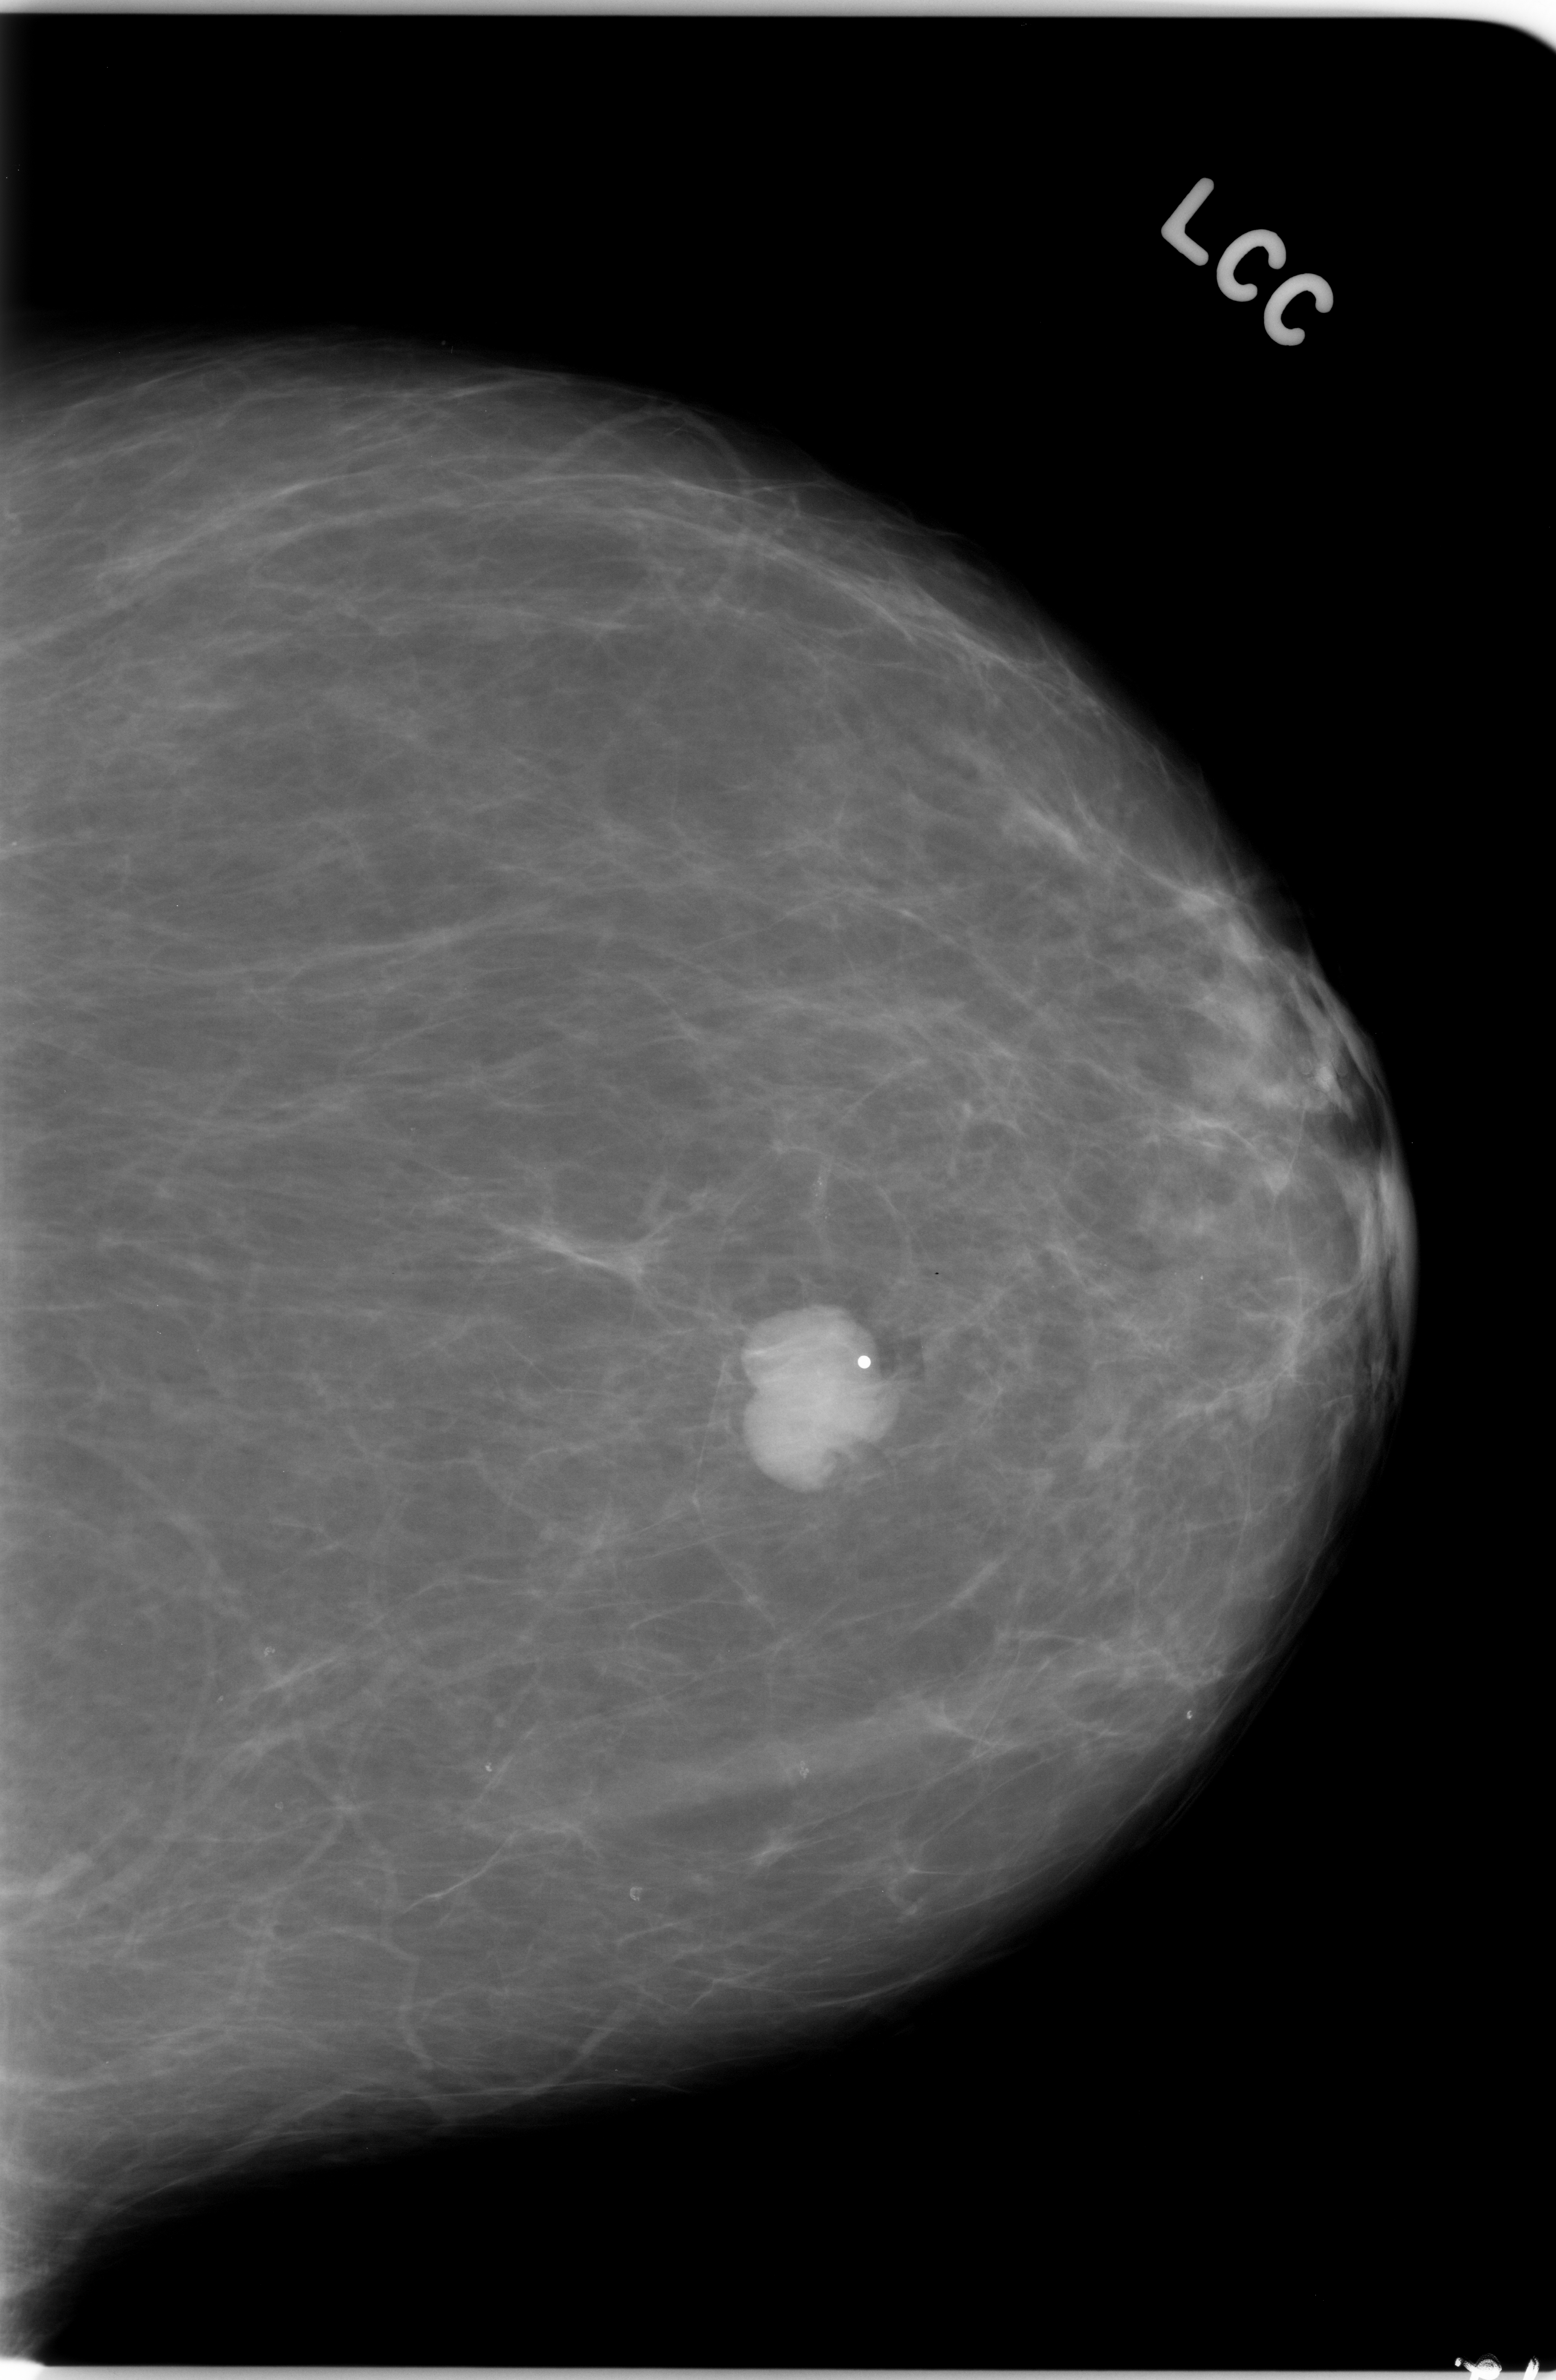
Scanned film-screen mammogram, left breast, craniocaudal (CC) view, breast composition: almost entirely fatty (BI-RADS density category 1 of 4).
Marked abnormality: mass, shape lobulated, margins circumscribed; BI-RADS assessment category 5; subtlety rating 5 on a 1 (subtle) to 5 (obvious) scale; pathology (as recorded): malignant.